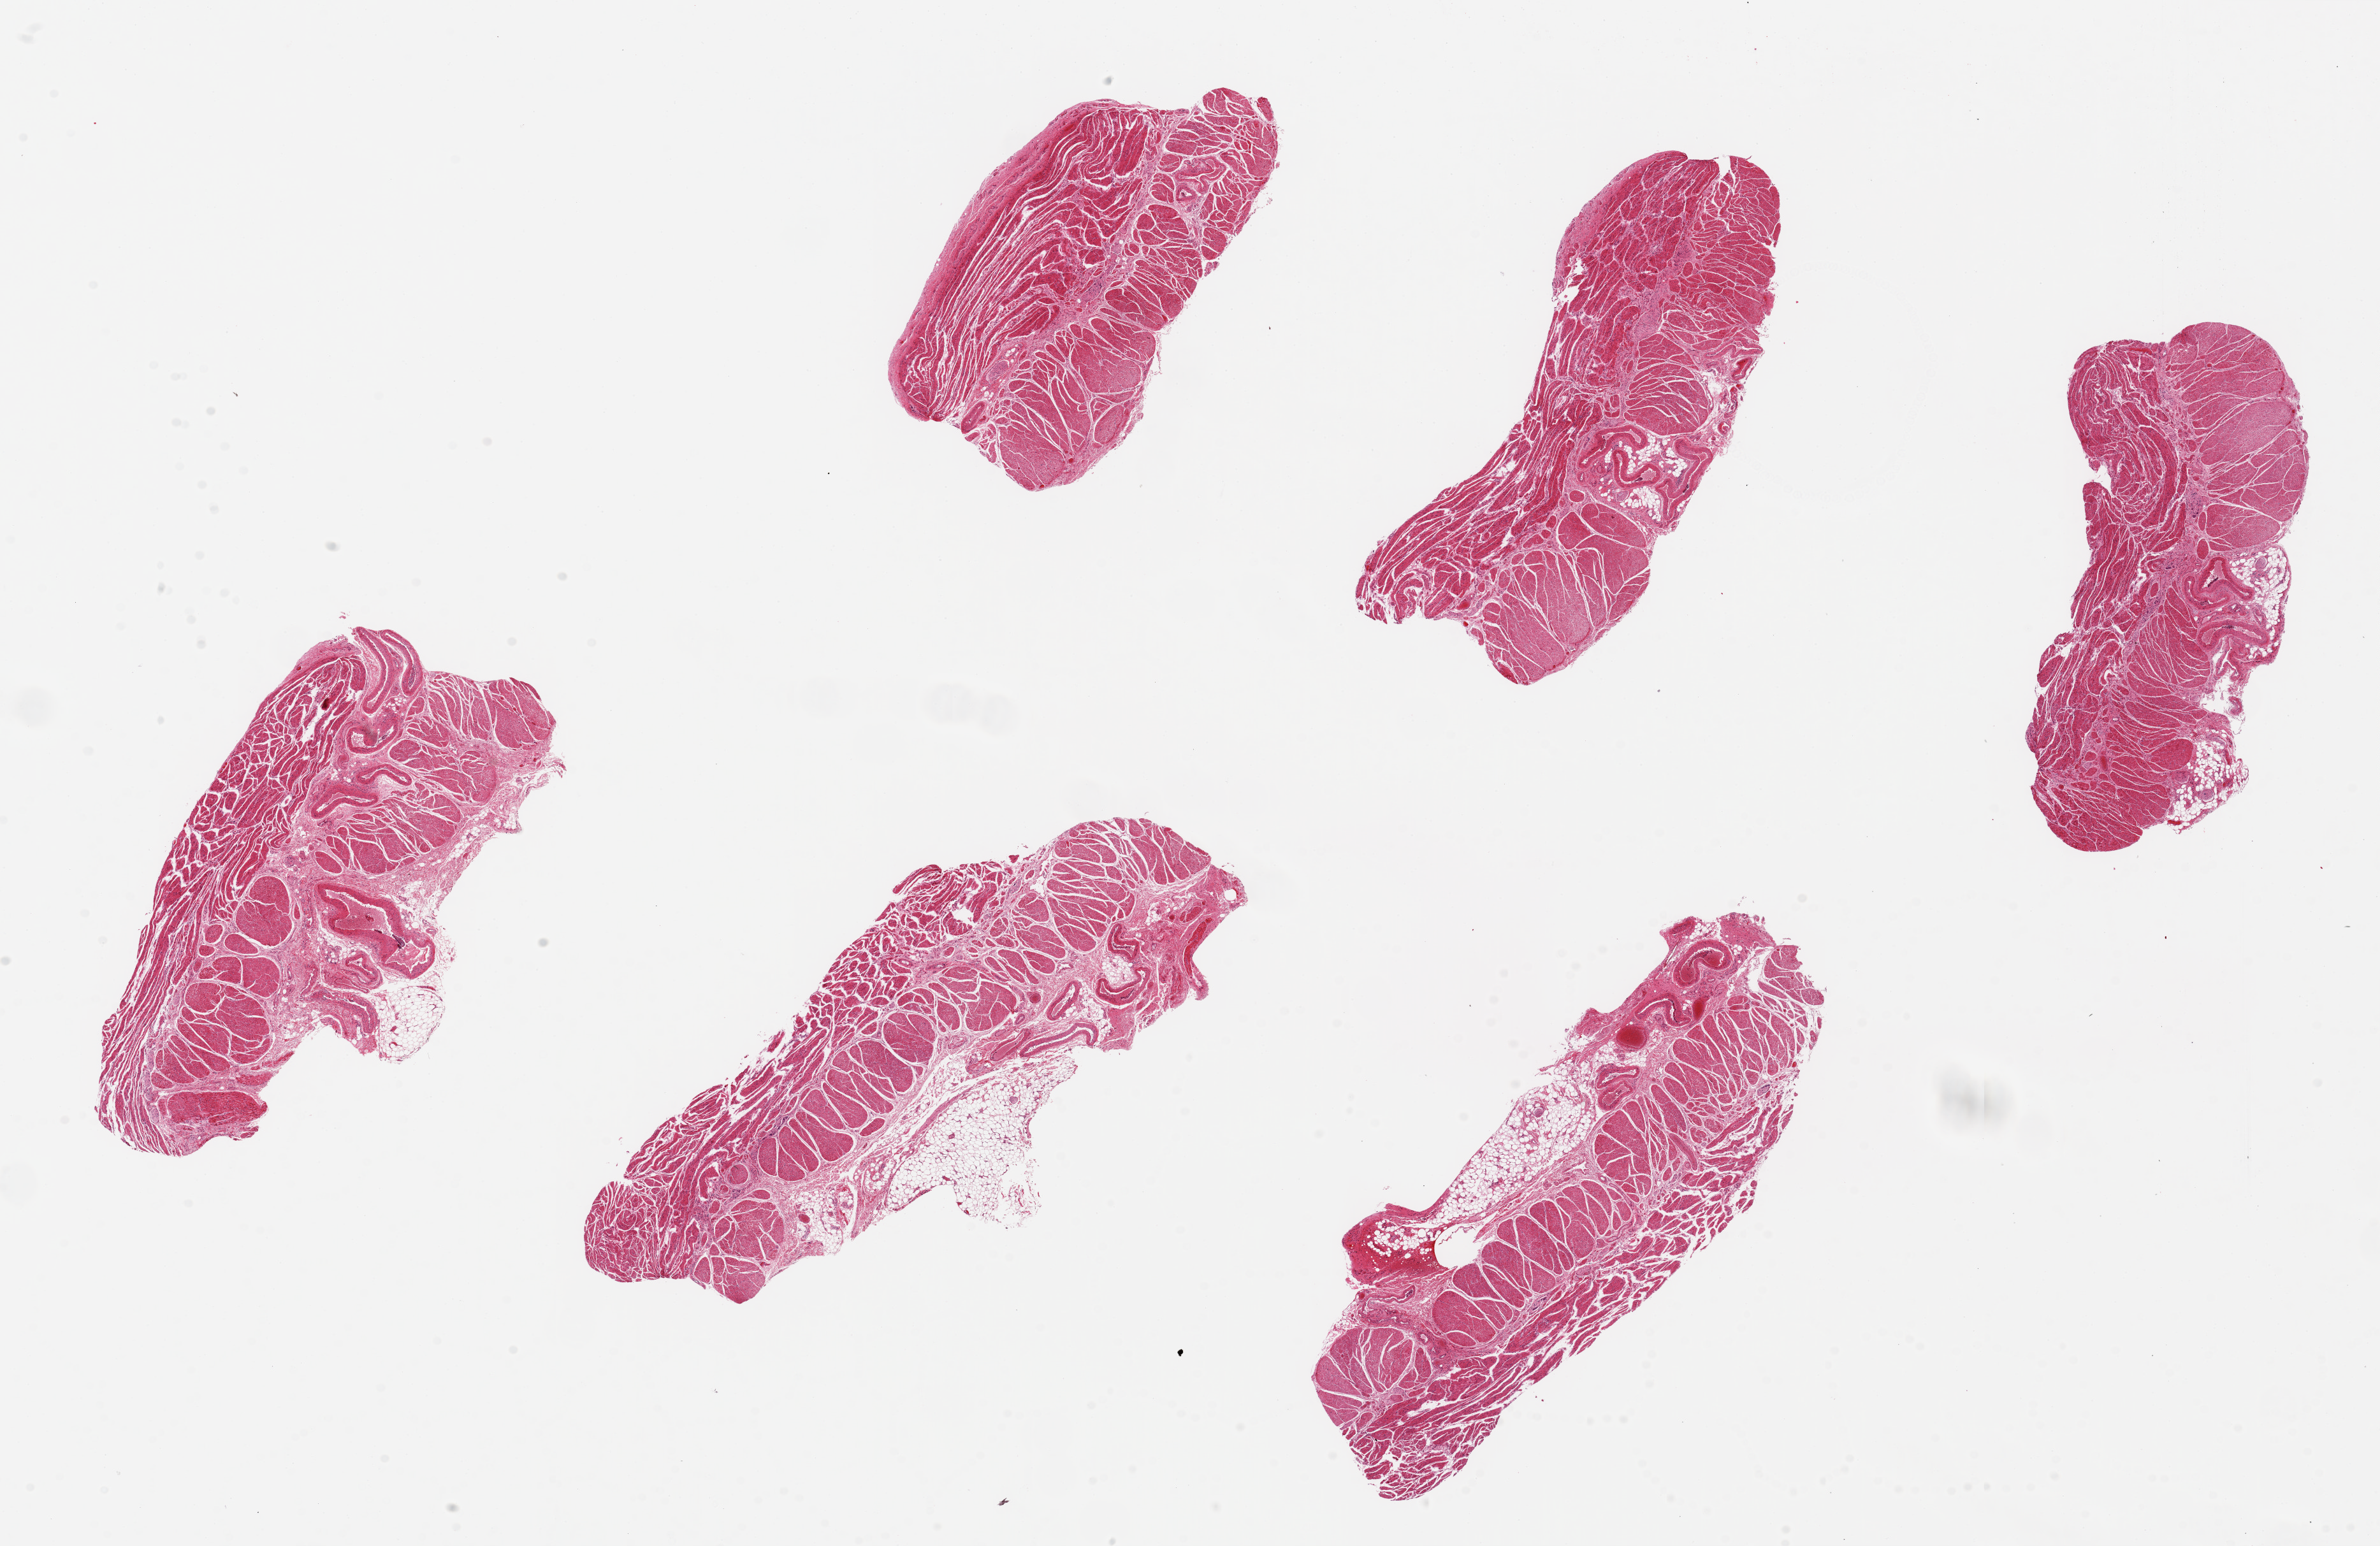
Whole-slide image, H&E stain — whole scanned area (about 29.5 x 19.2 mm) shown as a low-resolution overview. PAXgene-fixed, paraffin-embedded tissue. Target tissue: esophageal muscle. Tissue donor sample. Donor sex: male.
• reviewer comment on this tissue sample: 6 pieces, up to 9x4mm